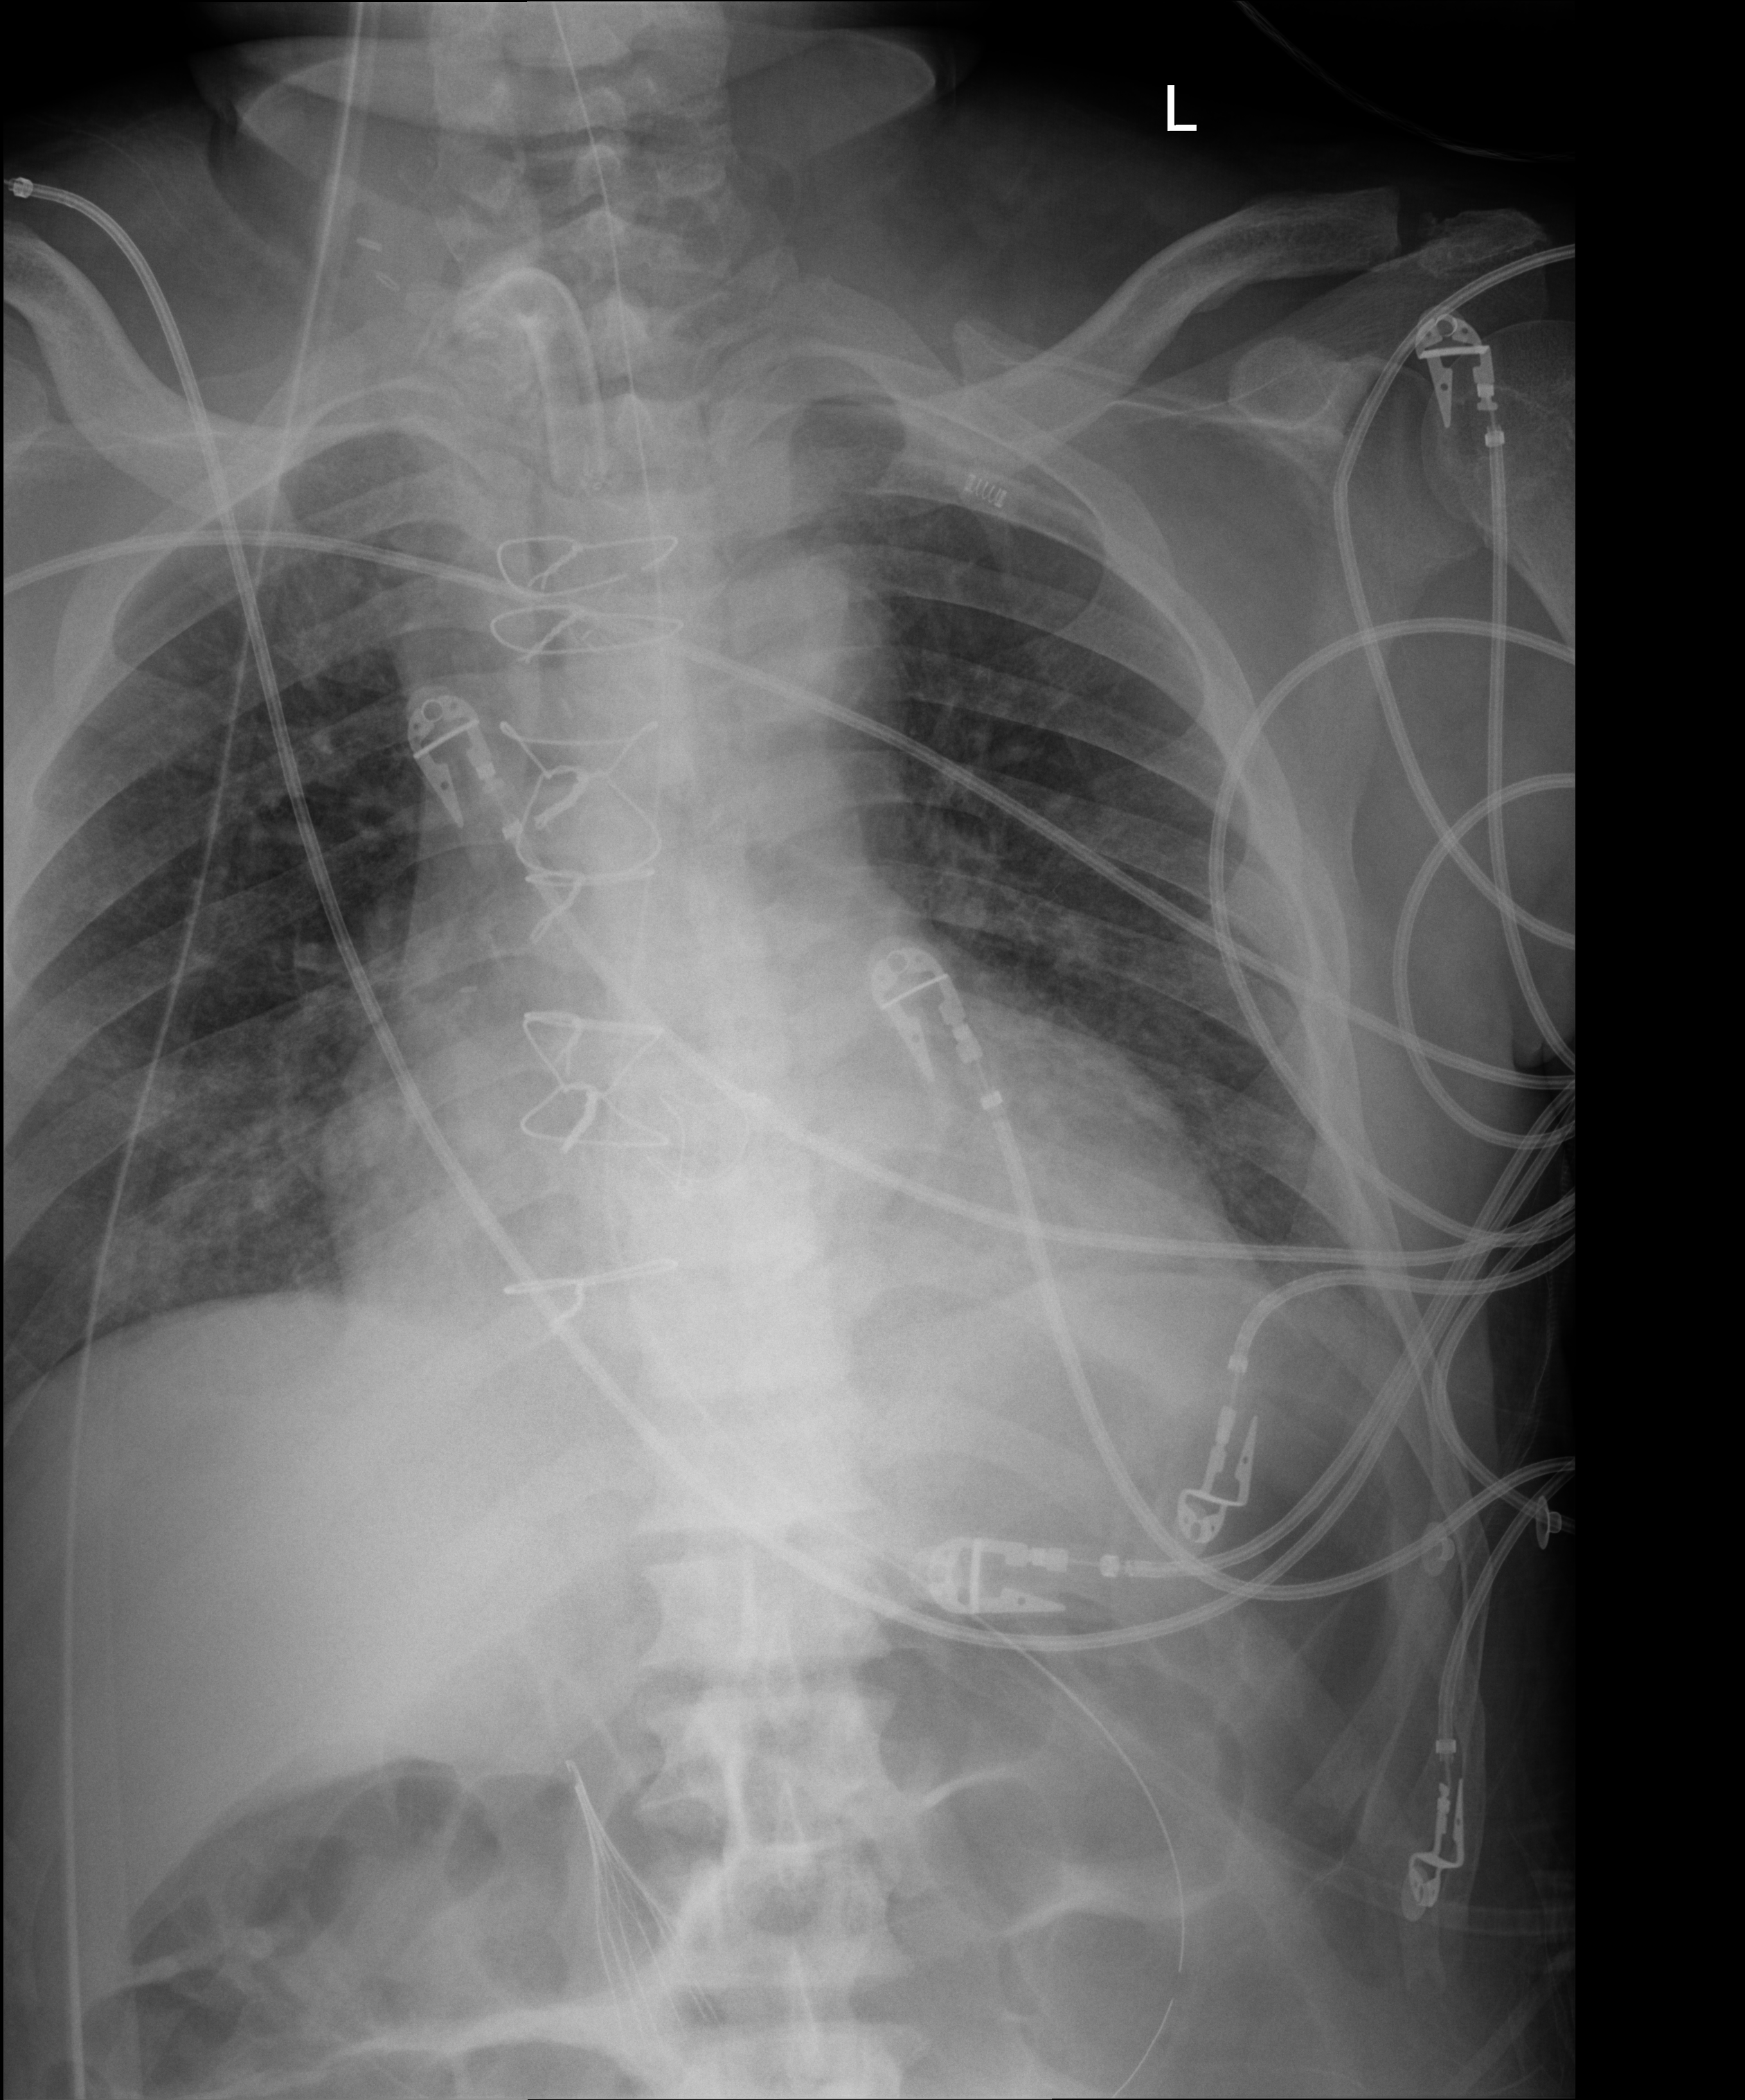
Bedside chest radiograph (digital radiography); anteroposterior (AP) projection. Male patient hospitalised with COVID-19, age 60–74 years.
From the hospital-stay record, not from the radiograph (when in the stay this image was taken is not recorded): admitted to intensive care during this hospital stay: yes; length of hospital stay: 50 days.